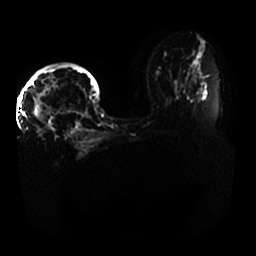
Breast MRI, one axial slice; position 20 of 33 along the scan axis; diffusion-weighted series; image 2 of 4 stored at this slice position (different b-values; order by instance number); 1.5 T; 256 × 256 image matrix, field of view 400 × 400 mm. Female patient.
Structures marked on this image (outlined manually by an expert reader):
- tumour on diffusion-weighted imaging: bounding box (x1, y1, x2, y2) in pixels: (36, 98, 55, 124)